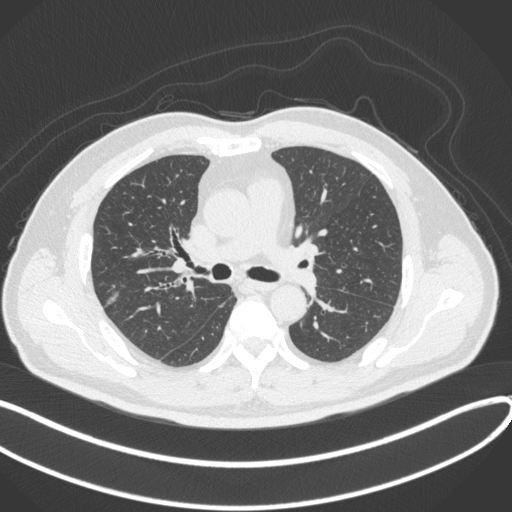
Chest CT, one axial slice; position 208 of 373 along the scan axis; 120 kVp; lung window (W 1500 / L -600 HU); 1 mm slice thickness; 512 × 512 image matrix. Male patient, age 60 years. Case-level facts recorded for this patient, not image findings: clinical TNM (as recorded): T1c N0 M0.
Outlined on this slice (bounding box drawn by a radiologist):
- lung tumour (recorded histology: adenocarcinoma): bounding box <101,280,130,311> (left, top, right, bottom; pixels)